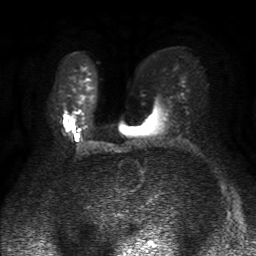
Breast MRI, one axial slice. Slice 31 of 50 in the series (ordered by position). Diffusion-weighted series; image 2 of 4 stored at this slice position (different b-values; order by instance number). 1.5 T. 4 mm slice thickness. 256 × 256 image matrix. Female patient.
Structures marked on this image (expert manual segmentation):
- tumour on diffusion-weighted imaging: bounding box <64,123,67,125> (left, top, right, bottom; pixels)